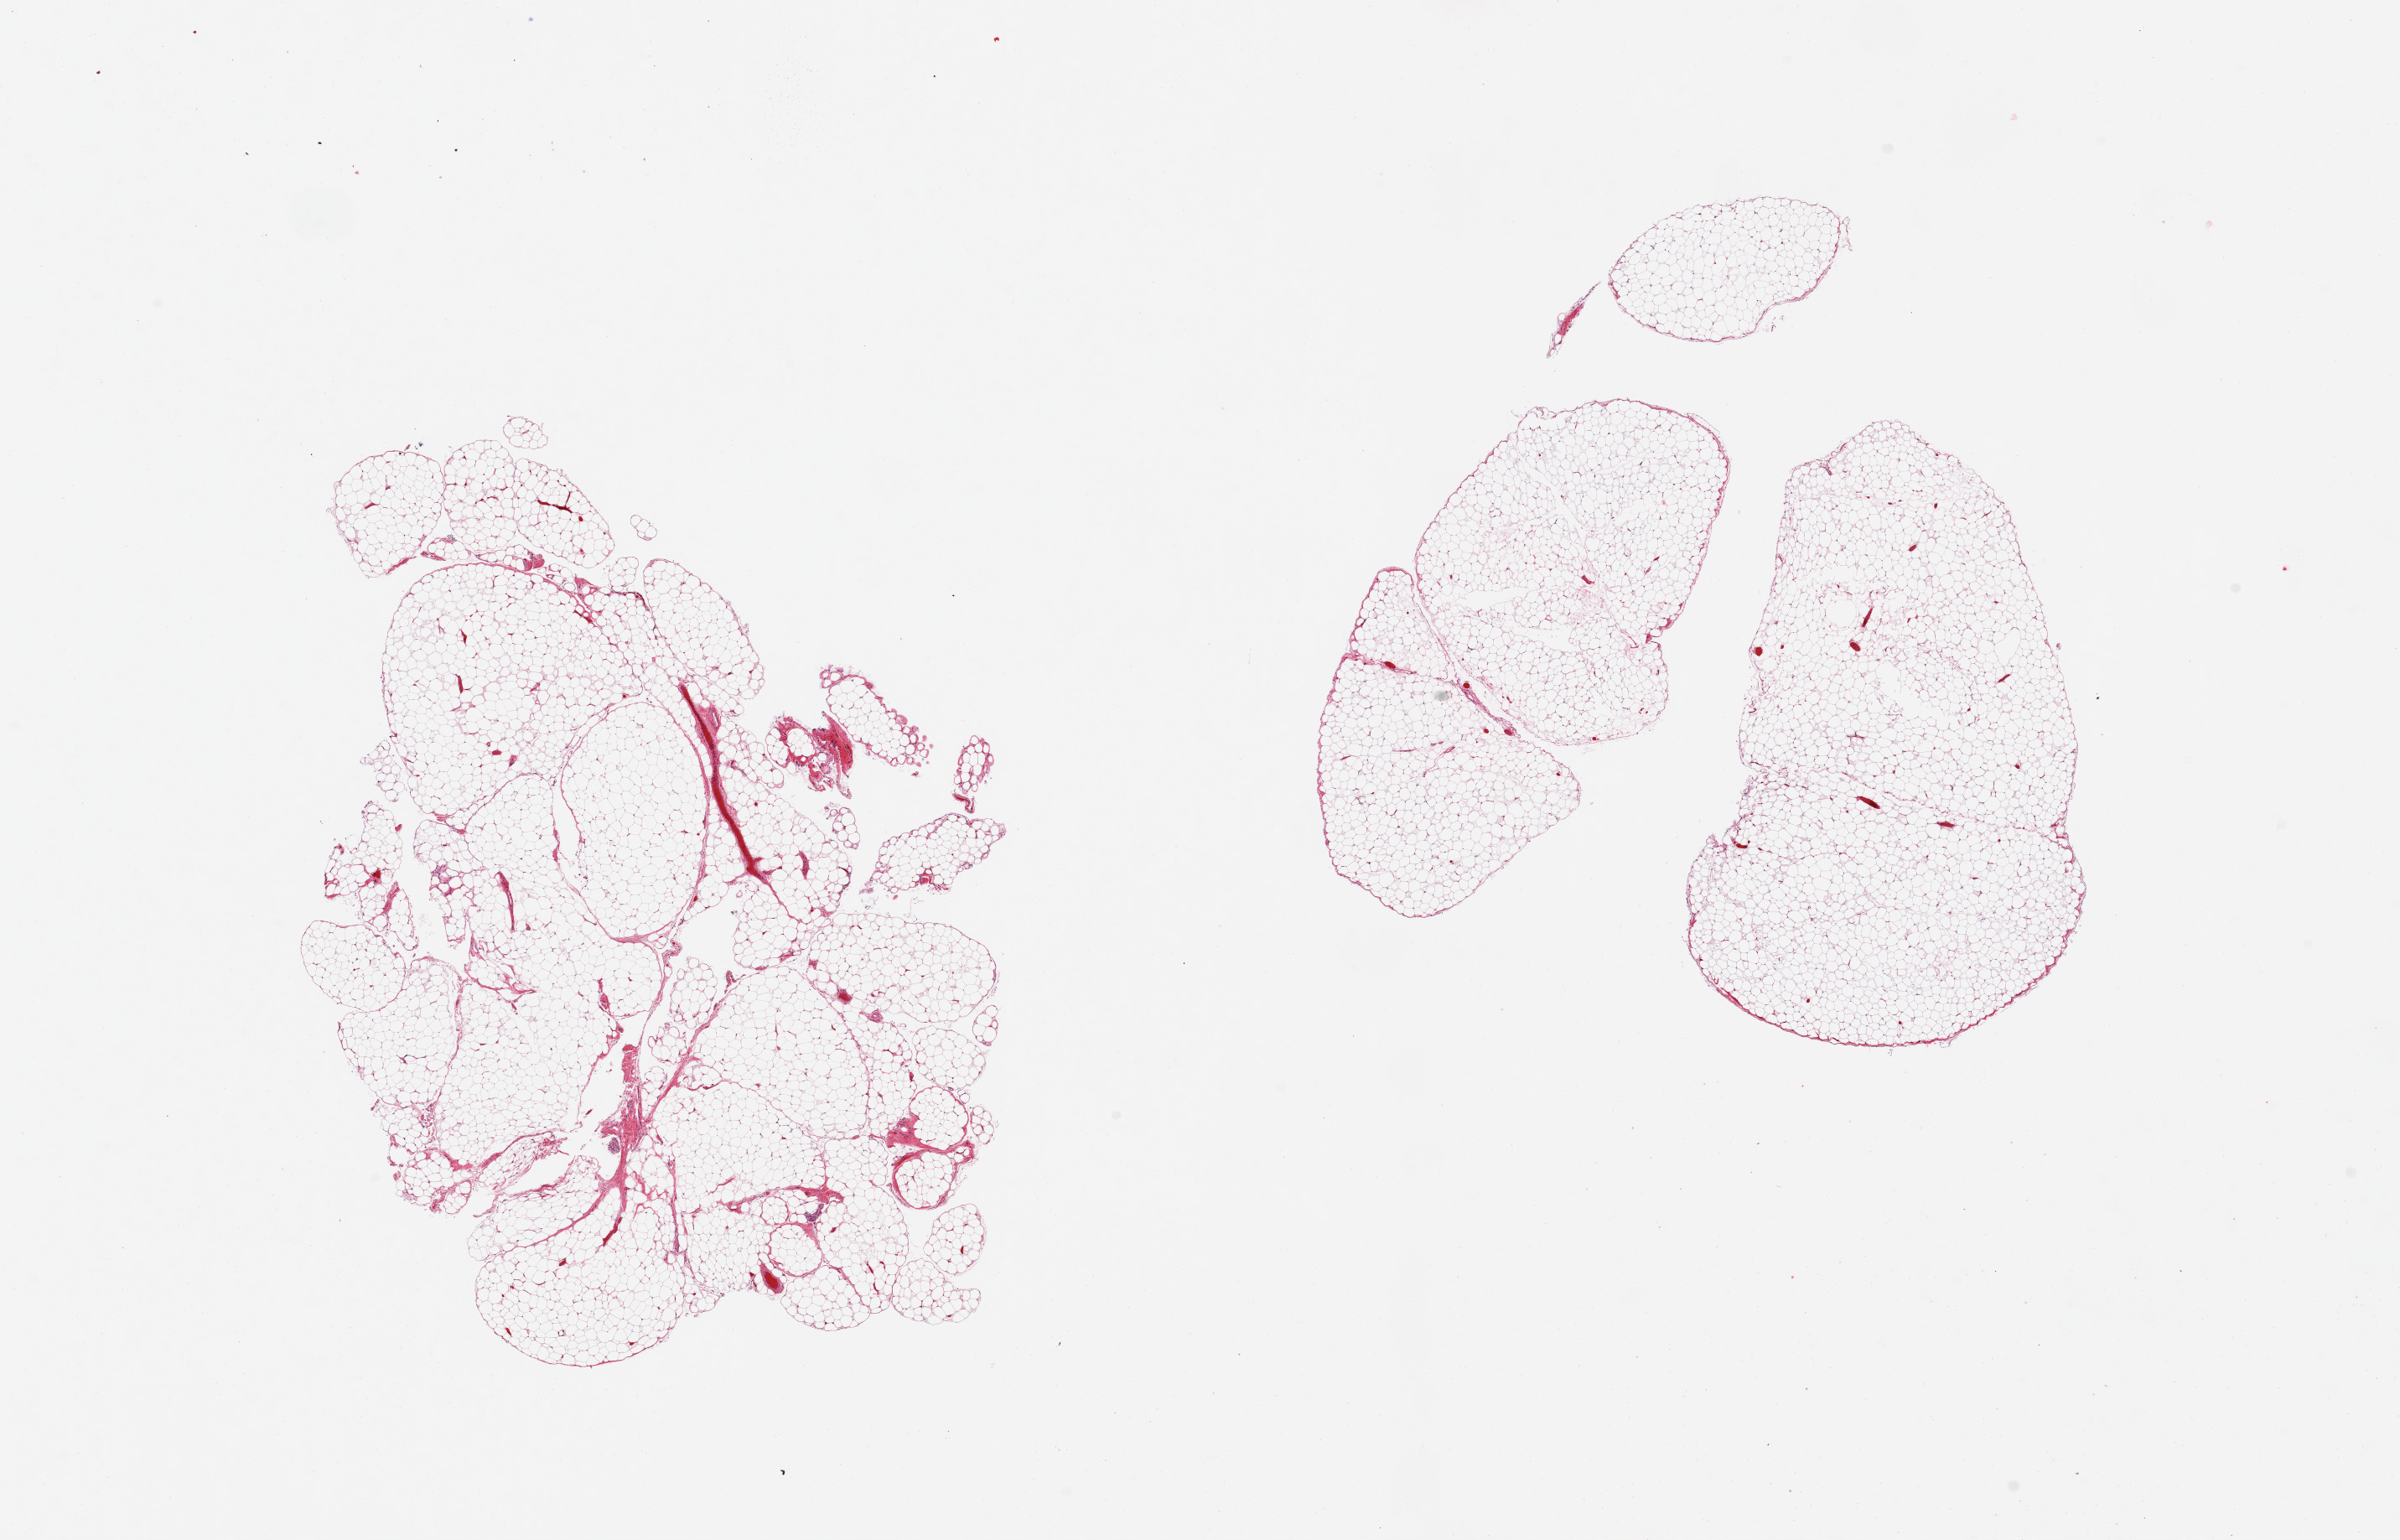
Whole-slide image, H&E stain, low-resolution overview of the scanned area, about 22.6 x 14.5 mm (acquisition: 20x scan), PAXgene-fixed, paraffin-embedded tissue, target tissue: omentum, tissue donor sample. Male donor.
* review note (as recorded): 2 pieces; lobulated fat with <5% fibrous content